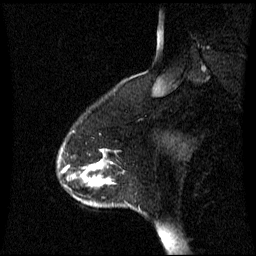
Breast MRI (dynamic contrast-enhanced), one sagittal slice; position 12 of 60 along the scan axis; dynamic contrast-enhanced series, image 2 of 3 at this slice position (ordered by acquisition); 1.5 T; TE 4.2 ms, TR 8.4 ms; 256 × 256 image matrix, field of view 240 × 240 mm. Female patient, age 45 years. Case-level facts recorded for this patient, not image findings: setting: breast cancer imaged before/during neoadjuvant chemotherapy; receptor status: HR-positive, HER2-negative.
Outlined on this slice (semi-automatically segmented with operator editing):
- analysis volume of interest (the breast-tissue region the enhancement analysis was run in; not a lesion): box from (x=58, y=148) to (x=113, y=207) px
- tumour enhancement mask (voxels above the 70 % enhancement threshold inside the analysis volume of interest): (x=92, y=162)–(x=113, y=185)